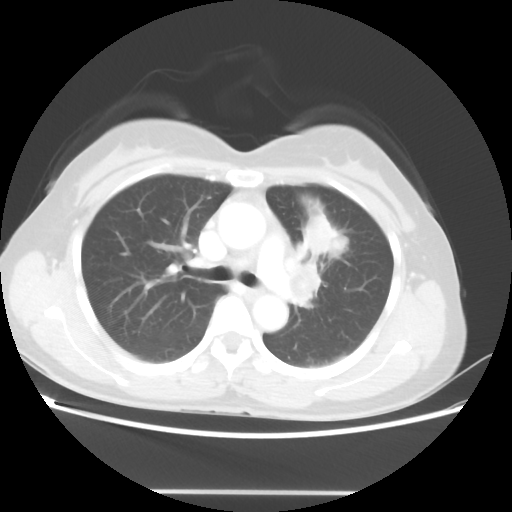
Chest CT, one axial slice. Position 29 of 46 along the scan axis. 100 kVp. Lung window (W 1500 / L -600 HU). 5 mm slice thickness. 512 × 512 image matrix, field of view 360 × 360 mm. Patient: female, 50 years. Case-level facts recorded for this patient, not image findings: clinical TNM (as recorded): T1c N1 M0; histopathological grade: G3.
Outlined on this slice (bounding box drawn by a radiologist):
- lung tumour (recorded histology: adenocarcinoma): bounding box <303,211,346,256> (left, top, right, bottom; pixels)